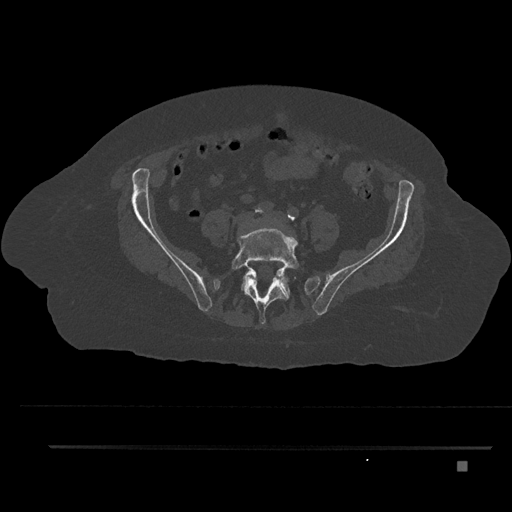
CT including the spine, one axial slice; position 38 of 797 along the scan axis; reconstruction kernel Br40s/3; bone window (W 1800 / L 400 HU); 0.5 mm slice thickness; 512 × 512 image matrix, field of view 437 × 437 mm. Patient: female, 76 years. Case-level facts recorded for this patient, not image findings: primary cancer: lung.
Structures marked on this image (semi-automatically segmented with operator editing):
- L4 vertebra: bounding box [x1, y1, x2, y2] px = [250, 276, 255, 279]
- L5 vertebra: [231, 220, 300, 325]